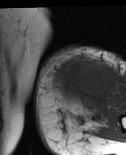
MRI of an extremity soft-tissue mass, one axial slice. Slice 21 of 86 in the series (ordered by position). MR volume resampled by the dataset authors to the PET/CT grid (not the native acquisition matrix). 126 × 155 image matrix, field of view 123 × 151 mm. Female patient. Case-level facts recorded for this patient, not image findings: histological type: pleiomorphic leiomyosarcoma; grade: high; site of the primary tumour: left biceps.
Outlined on this slice (expert contour drawn on MRI and transferred to this co-registered scan by the dataset authors):
- gross tumour volume including surrounding oedema: bounding box [x1, y1, x2, y2] px = [54, 58, 119, 112]
- gross tumour volume (mass): [54, 58, 117, 103]